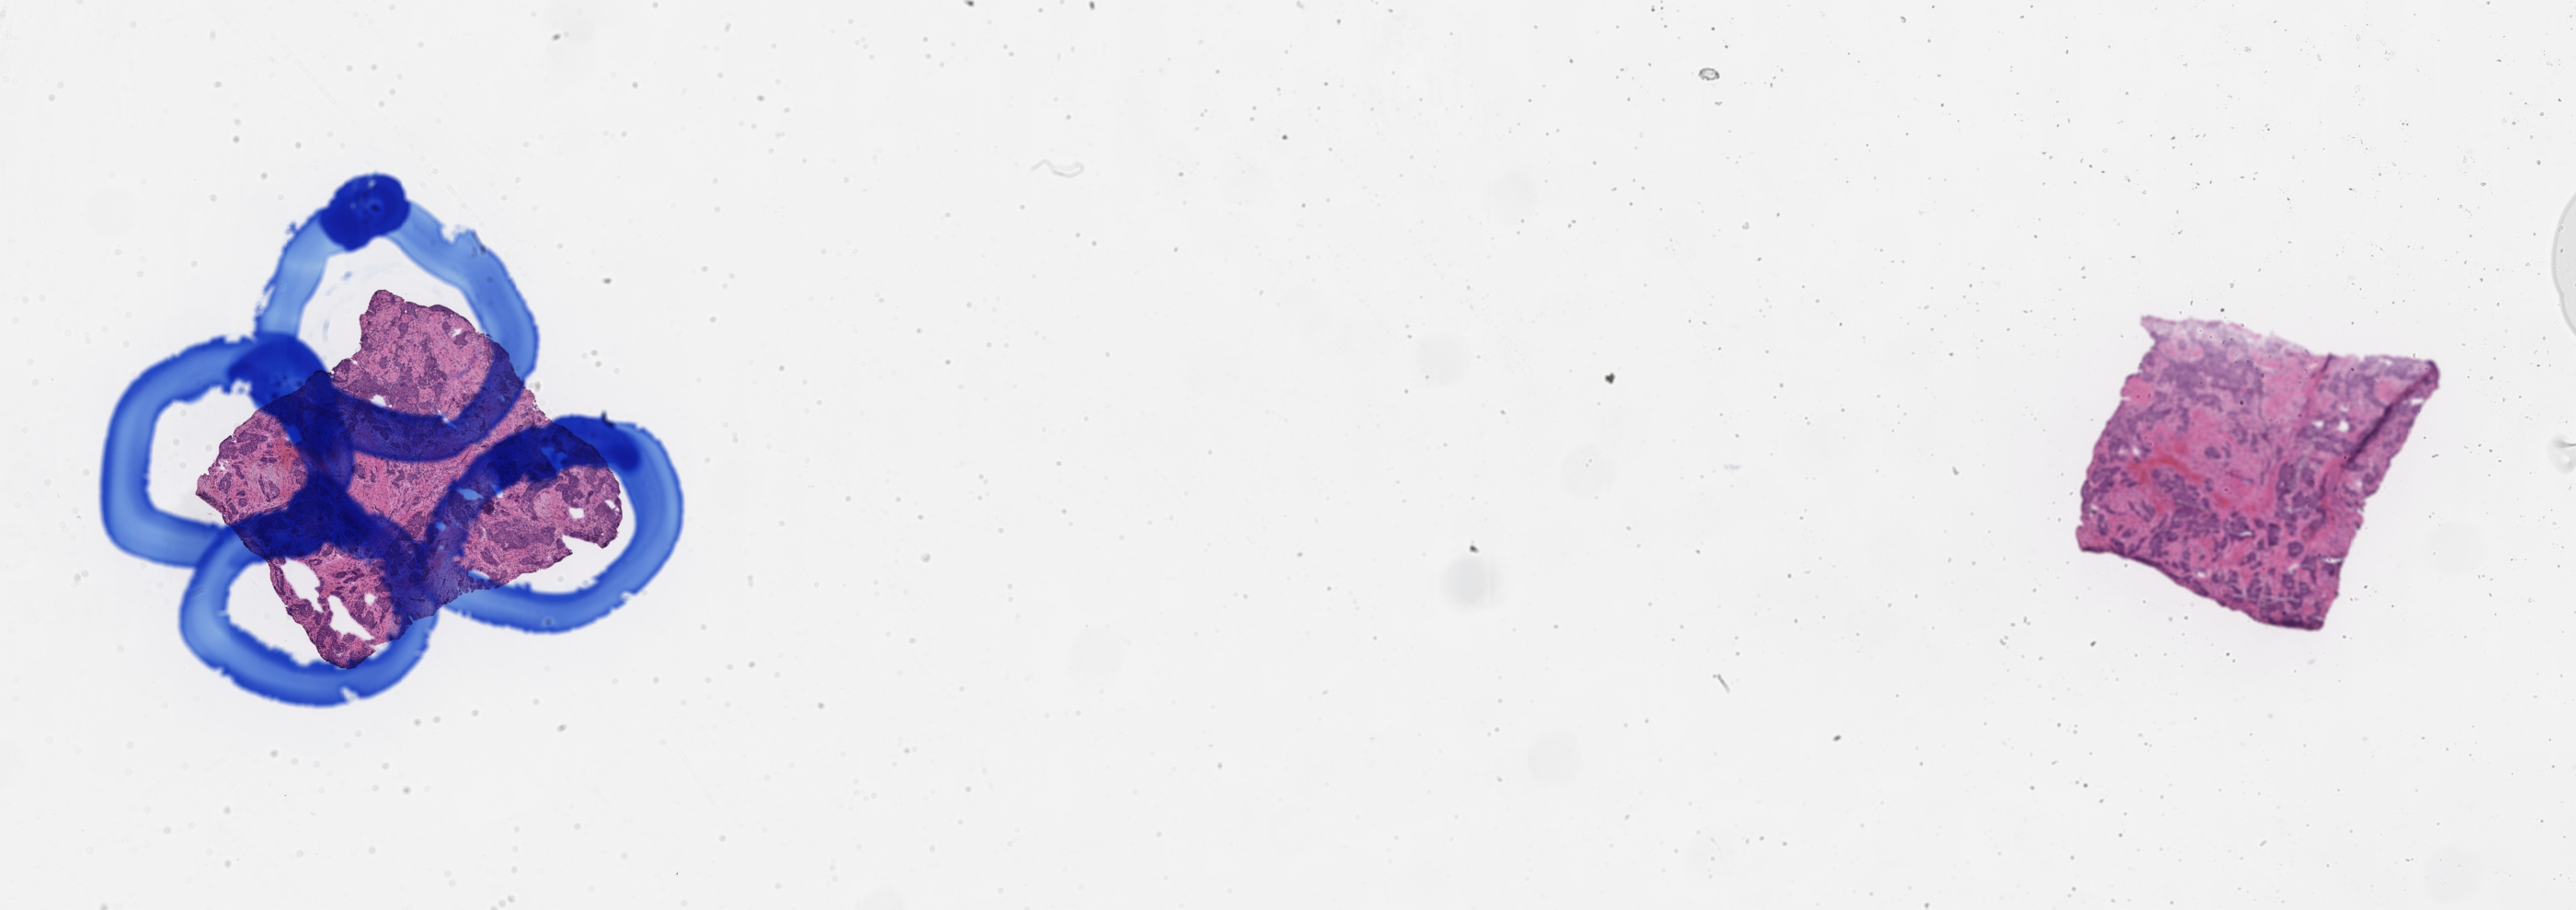
Digitized H&E-stained section, shown as a low-resolution overview of the whole scanned area (about 22.6 x 8.0 mm), frozen section (tissue freezing medium), specimen: primary tumor, anatomic site: breast (left). Female patient; age at initial diagnosis 42 years. Composition of this section per pathologist review: tumor cells 85%, tumor nuclei 85%, stromal cells 15%, necrosis 0%, normal cells 0%. Infiltration values recorded for this section: lymphocyte infiltration 4%, monocyte infiltration 1%, neutrophil infiltration 6%.
Diagnosis: Infiltrating duct carcinoma, NOS.